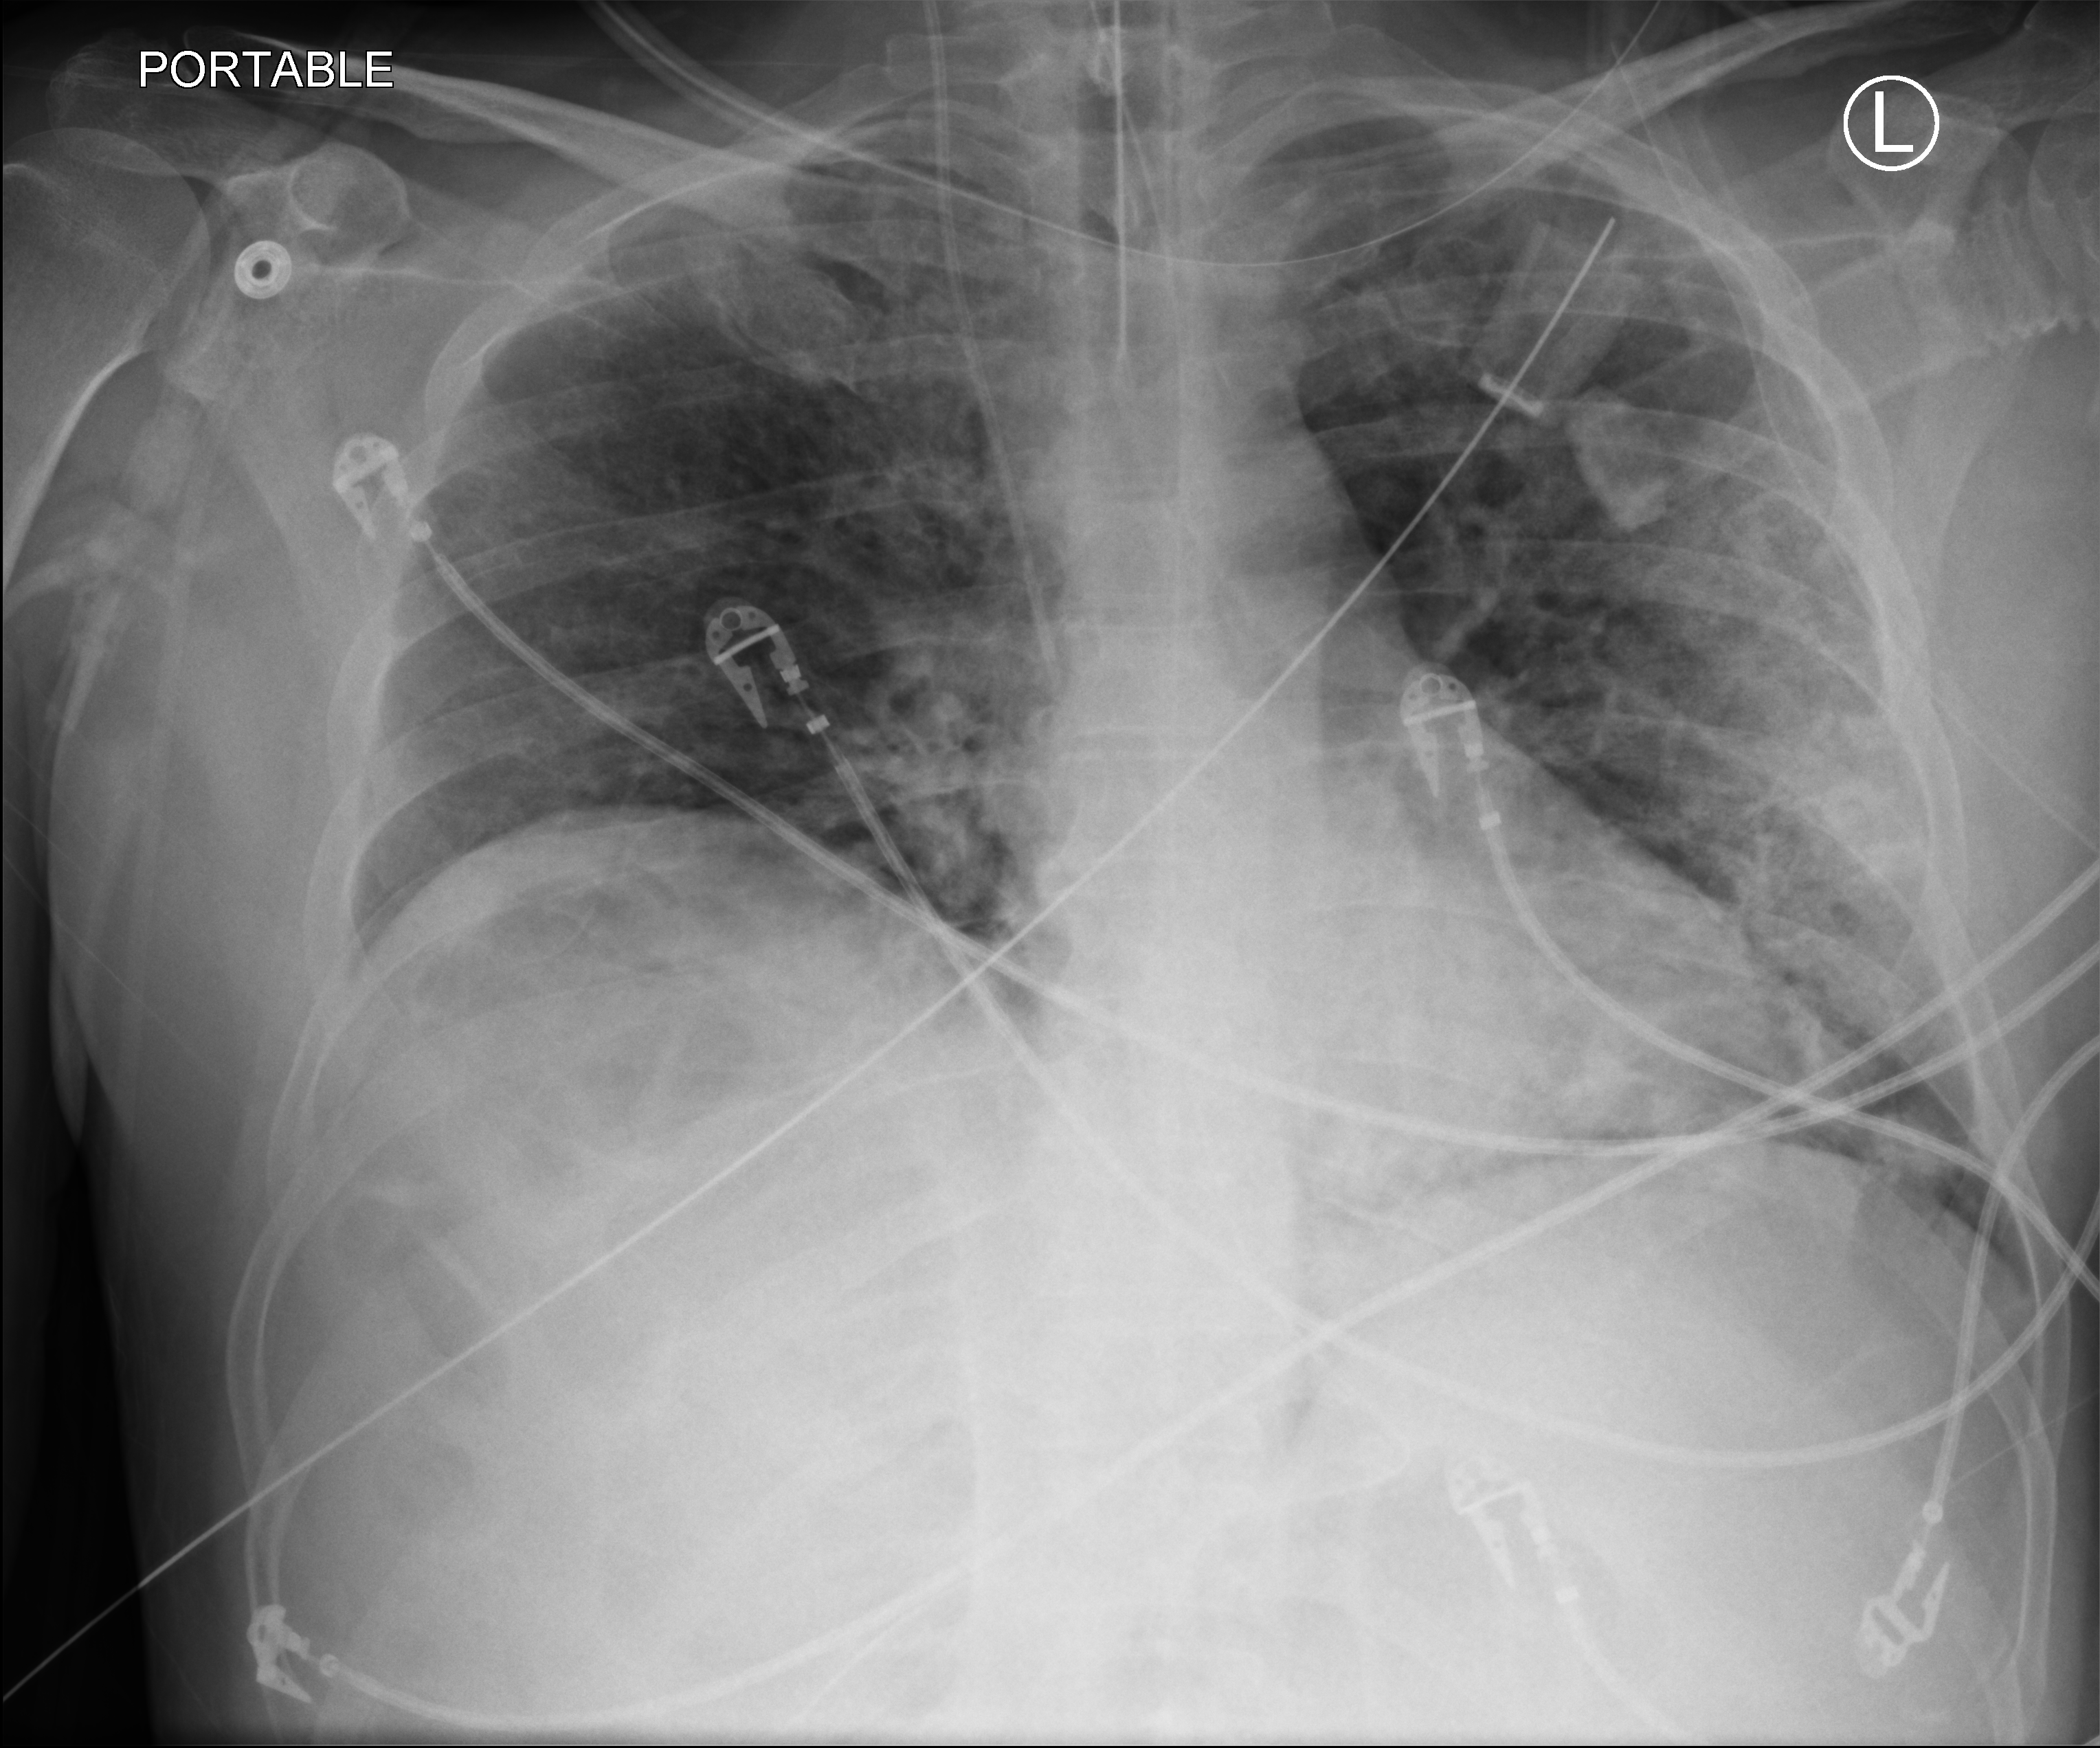
Bedside chest radiograph (computed radiography), anteroposterior (AP) projection. Male patient hospitalised with COVID-19, age 18–59 years.
From the hospital-stay record, not from the radiograph (when in the stay this image was taken is not recorded):
- mechanically ventilated during this hospital stay: yes
- admitted to intensive care during this hospital stay: yes